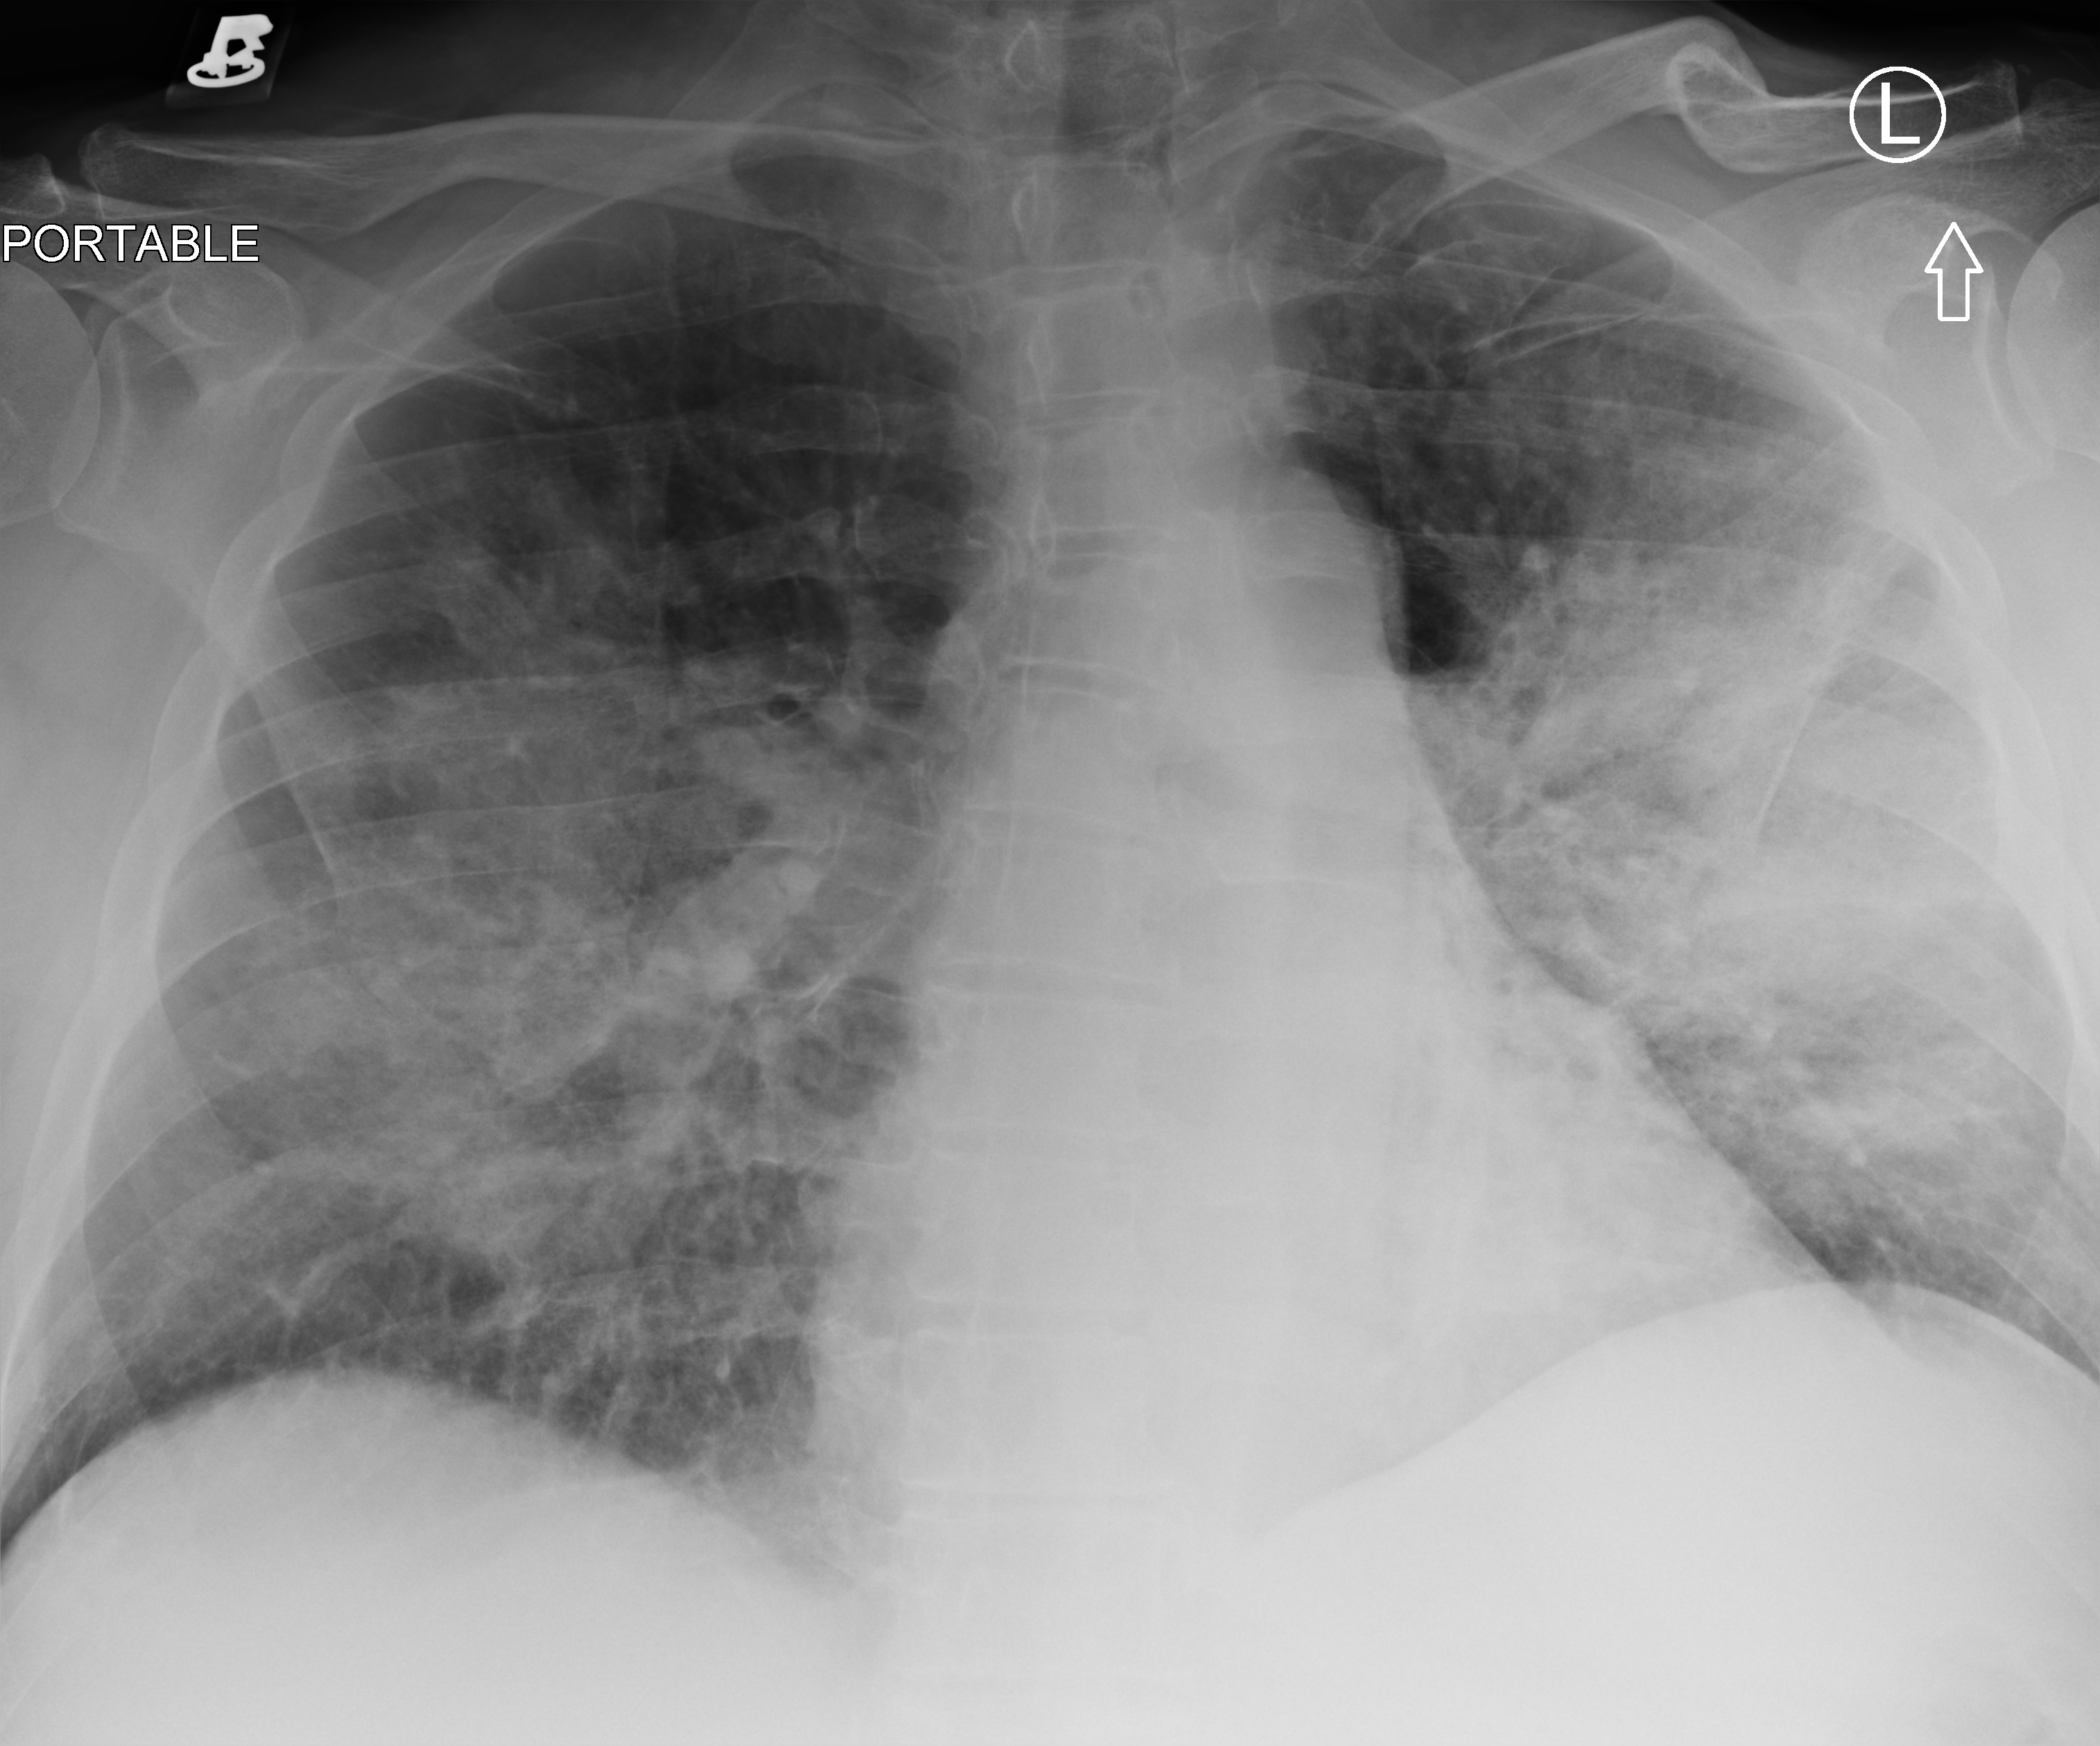
Chest X-ray (portable); anteroposterior (AP) projection. Patient hospitalised with COVID-19; male, aged 60–74 years.
From the hospital-stay record, not from the radiograph (when in the stay this image was taken is not recorded):
- COPD (admission record): no
- admitted to intensive care during this hospital stay: no
- mechanically ventilated during this hospital stay: no